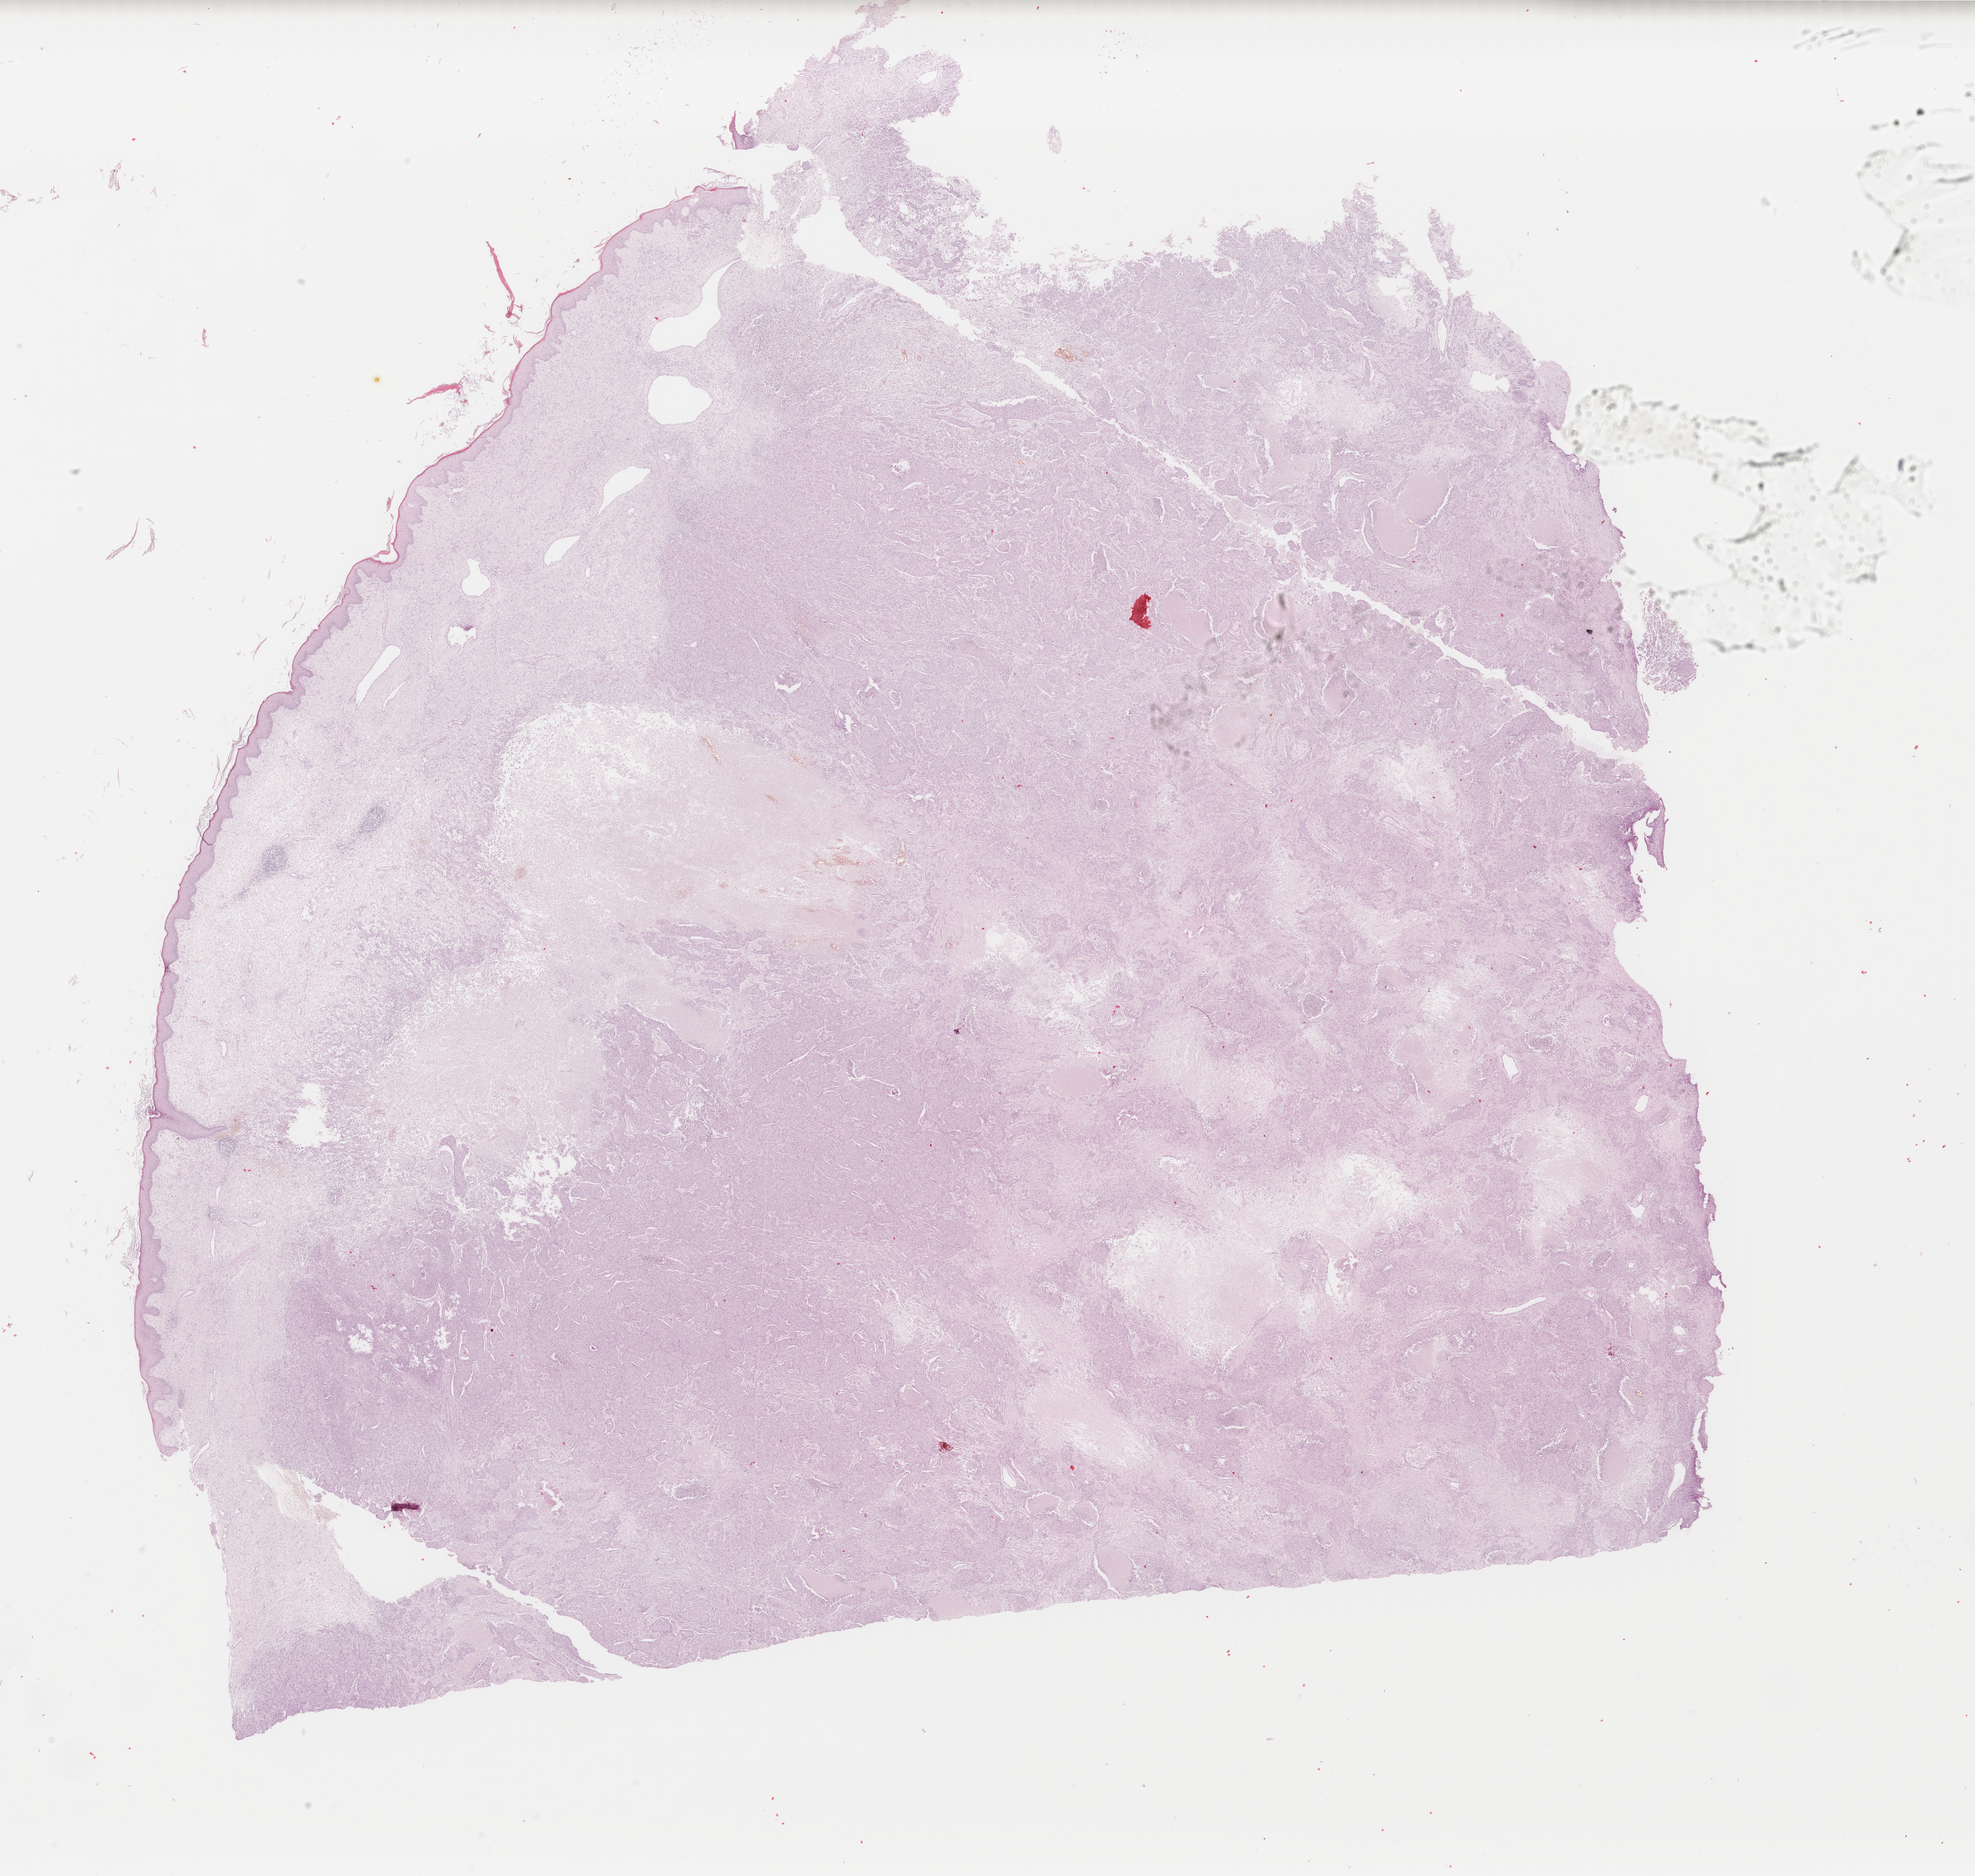
H&E whole-slide image — shown as a low-resolution overview of the whole scanned area (about 24.3 x 23.1 mm), formalin-fixed paraffin-embedded (FFPE) diagnostic section, sample: primary tumour, breast. Female patient; age at initial diagnosis 60 years.
Diagnosis: Infiltrating duct carcinoma, NOS. Laterality: left.